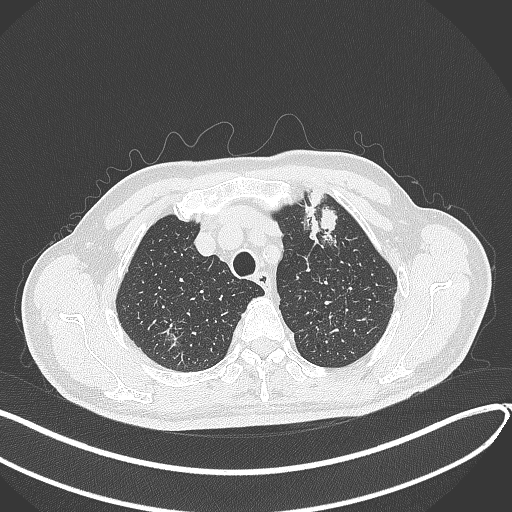
Chest CT, one axial slice; slice 349 of 459 in the series (ordered by position); reconstruction kernel B70f; lung window (W 1500 / L -600 HU); 1 mm slice thickness; 512 × 512 image matrix, field of view 400 × 400 mm. Male patient, age 74 years. Case-level facts recorded for this patient, not image findings: clinical TNM (as recorded): T2b N0 M1c.
Outlined on this slice (rectangle marked by the reading radiologist):
- lung tumour (recorded histology: adenocarcinoma): box from (x=301, y=186) to (x=341, y=249) px